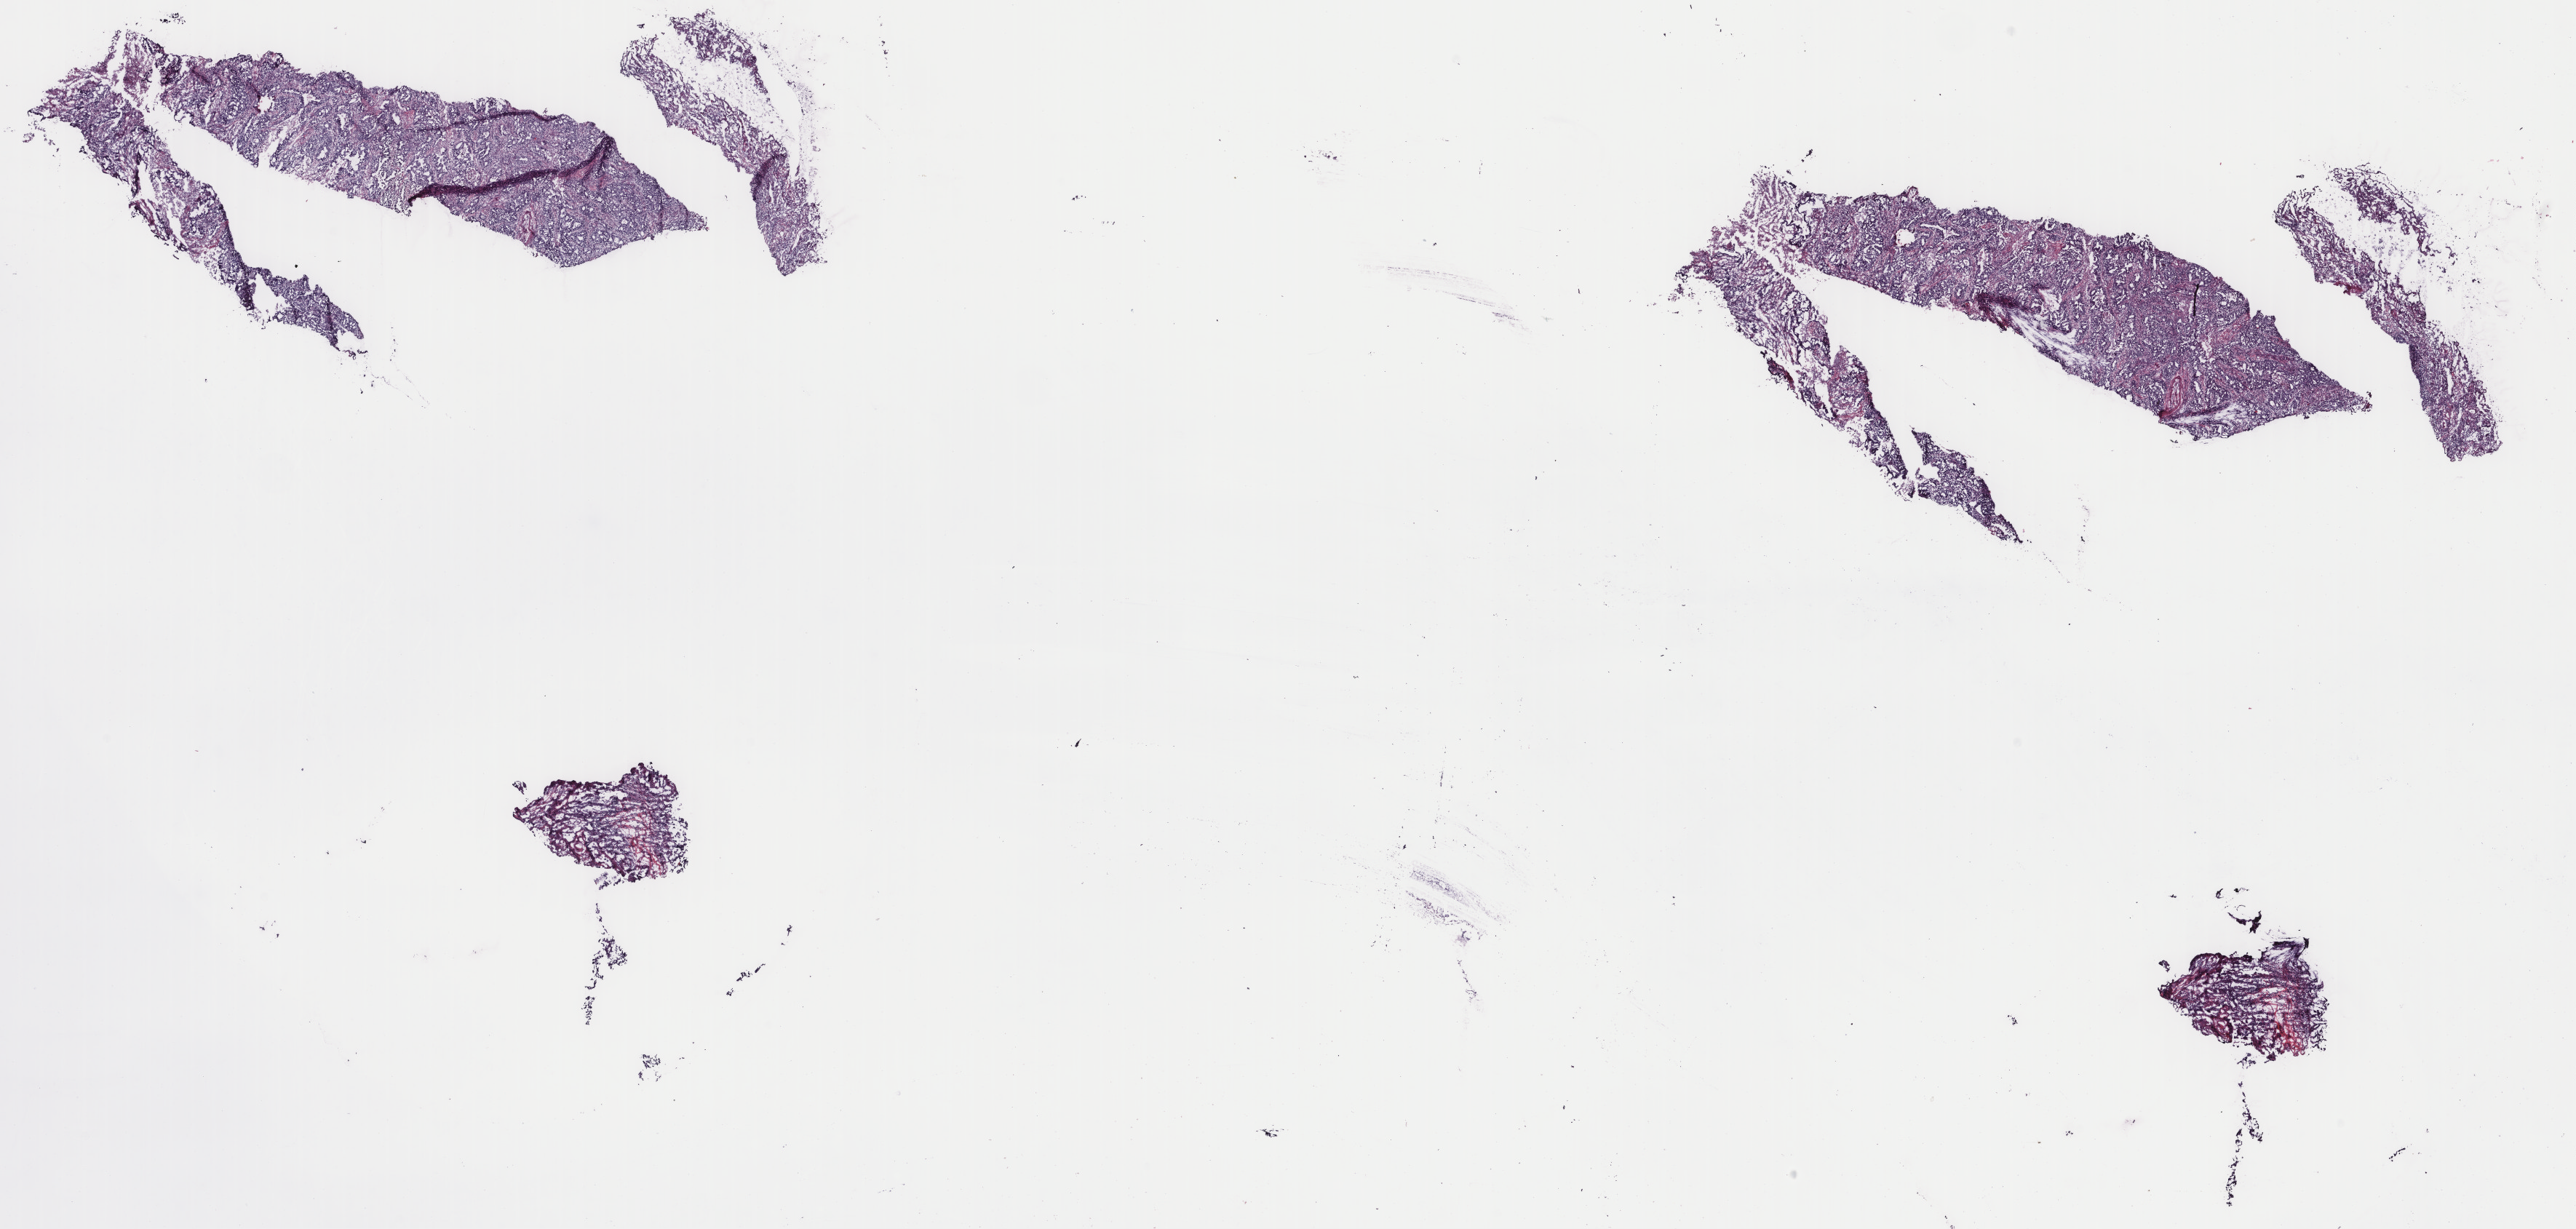
Digitized Hematoxylin and eosin (H&E) stained tissue section (whole slide), shown as a low-resolution overview of the whole scanned area (about 28.1 x 13.4 mm); frozen section from the top of the tissue portion; lung, primary tumour sample. Male patient. Slide review estimates, as recorded: tumour cells 100%, tumour nuclei 65%, normal cells 0%, stromal cells 0%, necrosis 0%. Infiltration values recorded for this section: lymphocyte infiltration 0%, monocyte infiltration 0%, neutrophil infiltration 0%.
AJCC pathologic stage: IA (7th edition). Diagnosis: Adenocarcinoma, NOS (lower lobe, lung). Laterality: right. TNM: T1b N0 MX.